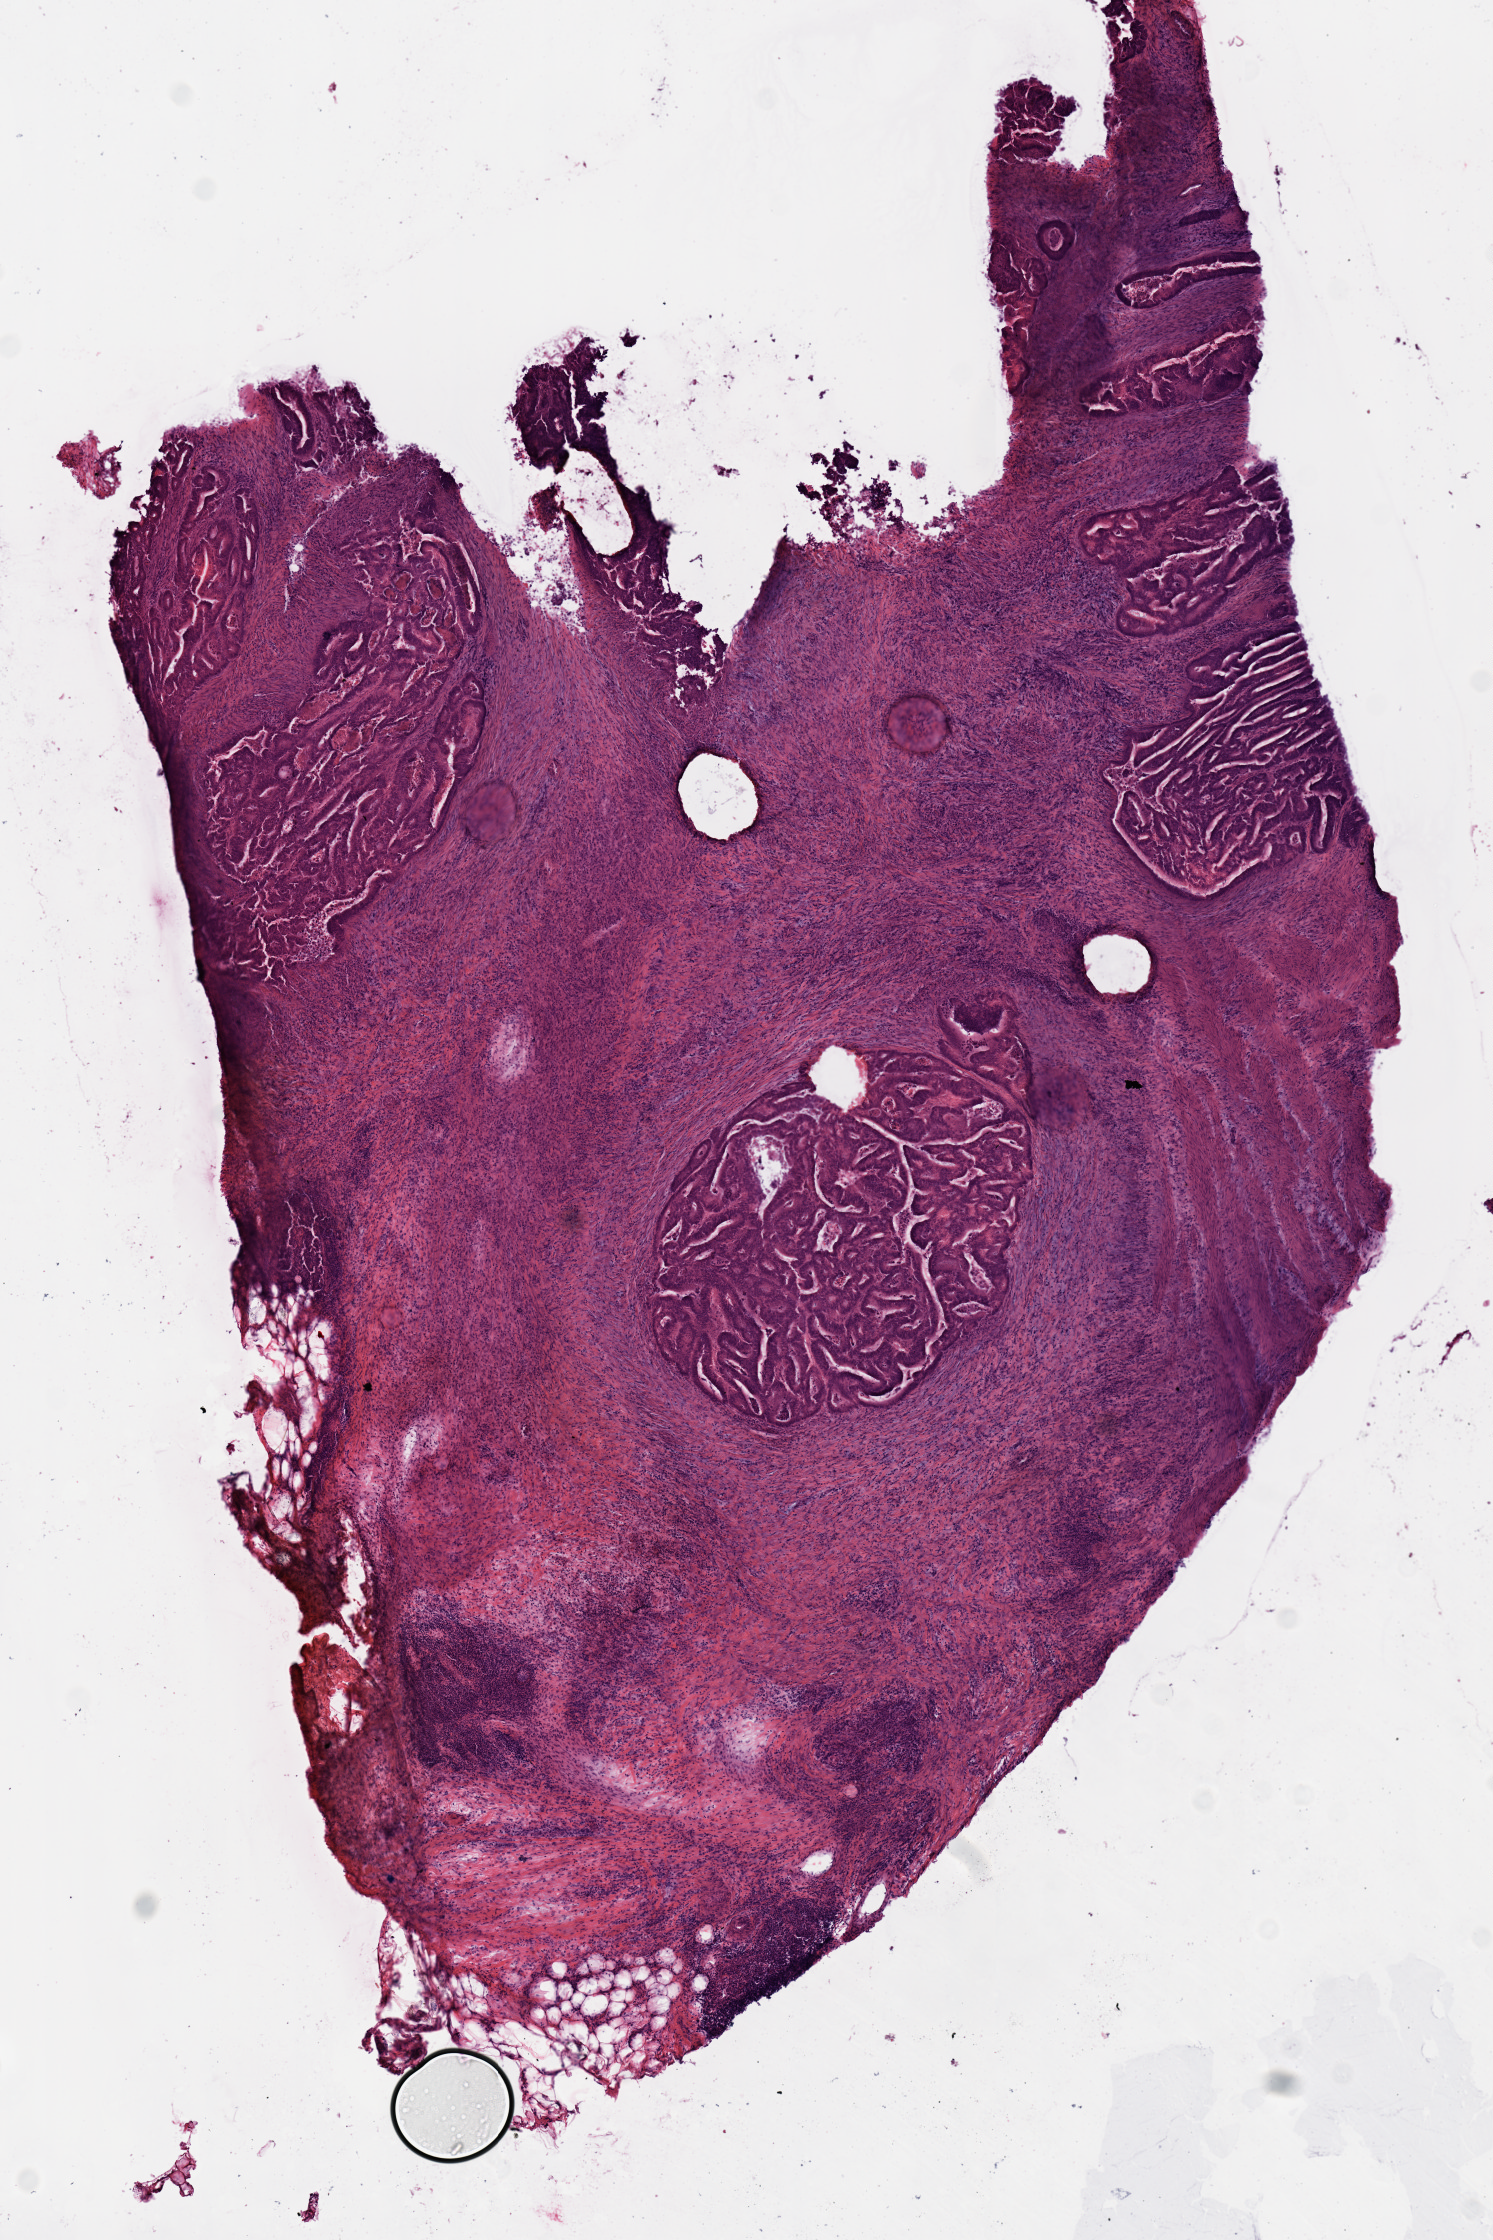
Whole-slide histology image, H&E — whole scanned area (about 5.9 x 8.9 mm, slide scanned at 20x) shown as a low-resolution overview, frozen section, rectum, primary tumour sample. Male, age 63 years at initial diagnosis. Slide review estimates, as recorded: tumour cells 50%, tumour nuclei 75%, normal cells 0%, stromal cells 35%, necrosis 15%.
Pathologic diagnosis: Tubular adenocarcinoma. AJCC pathologic stage: IIC (7th edition). Lymph nodes positive (case pathology): 0 of 16 examined.